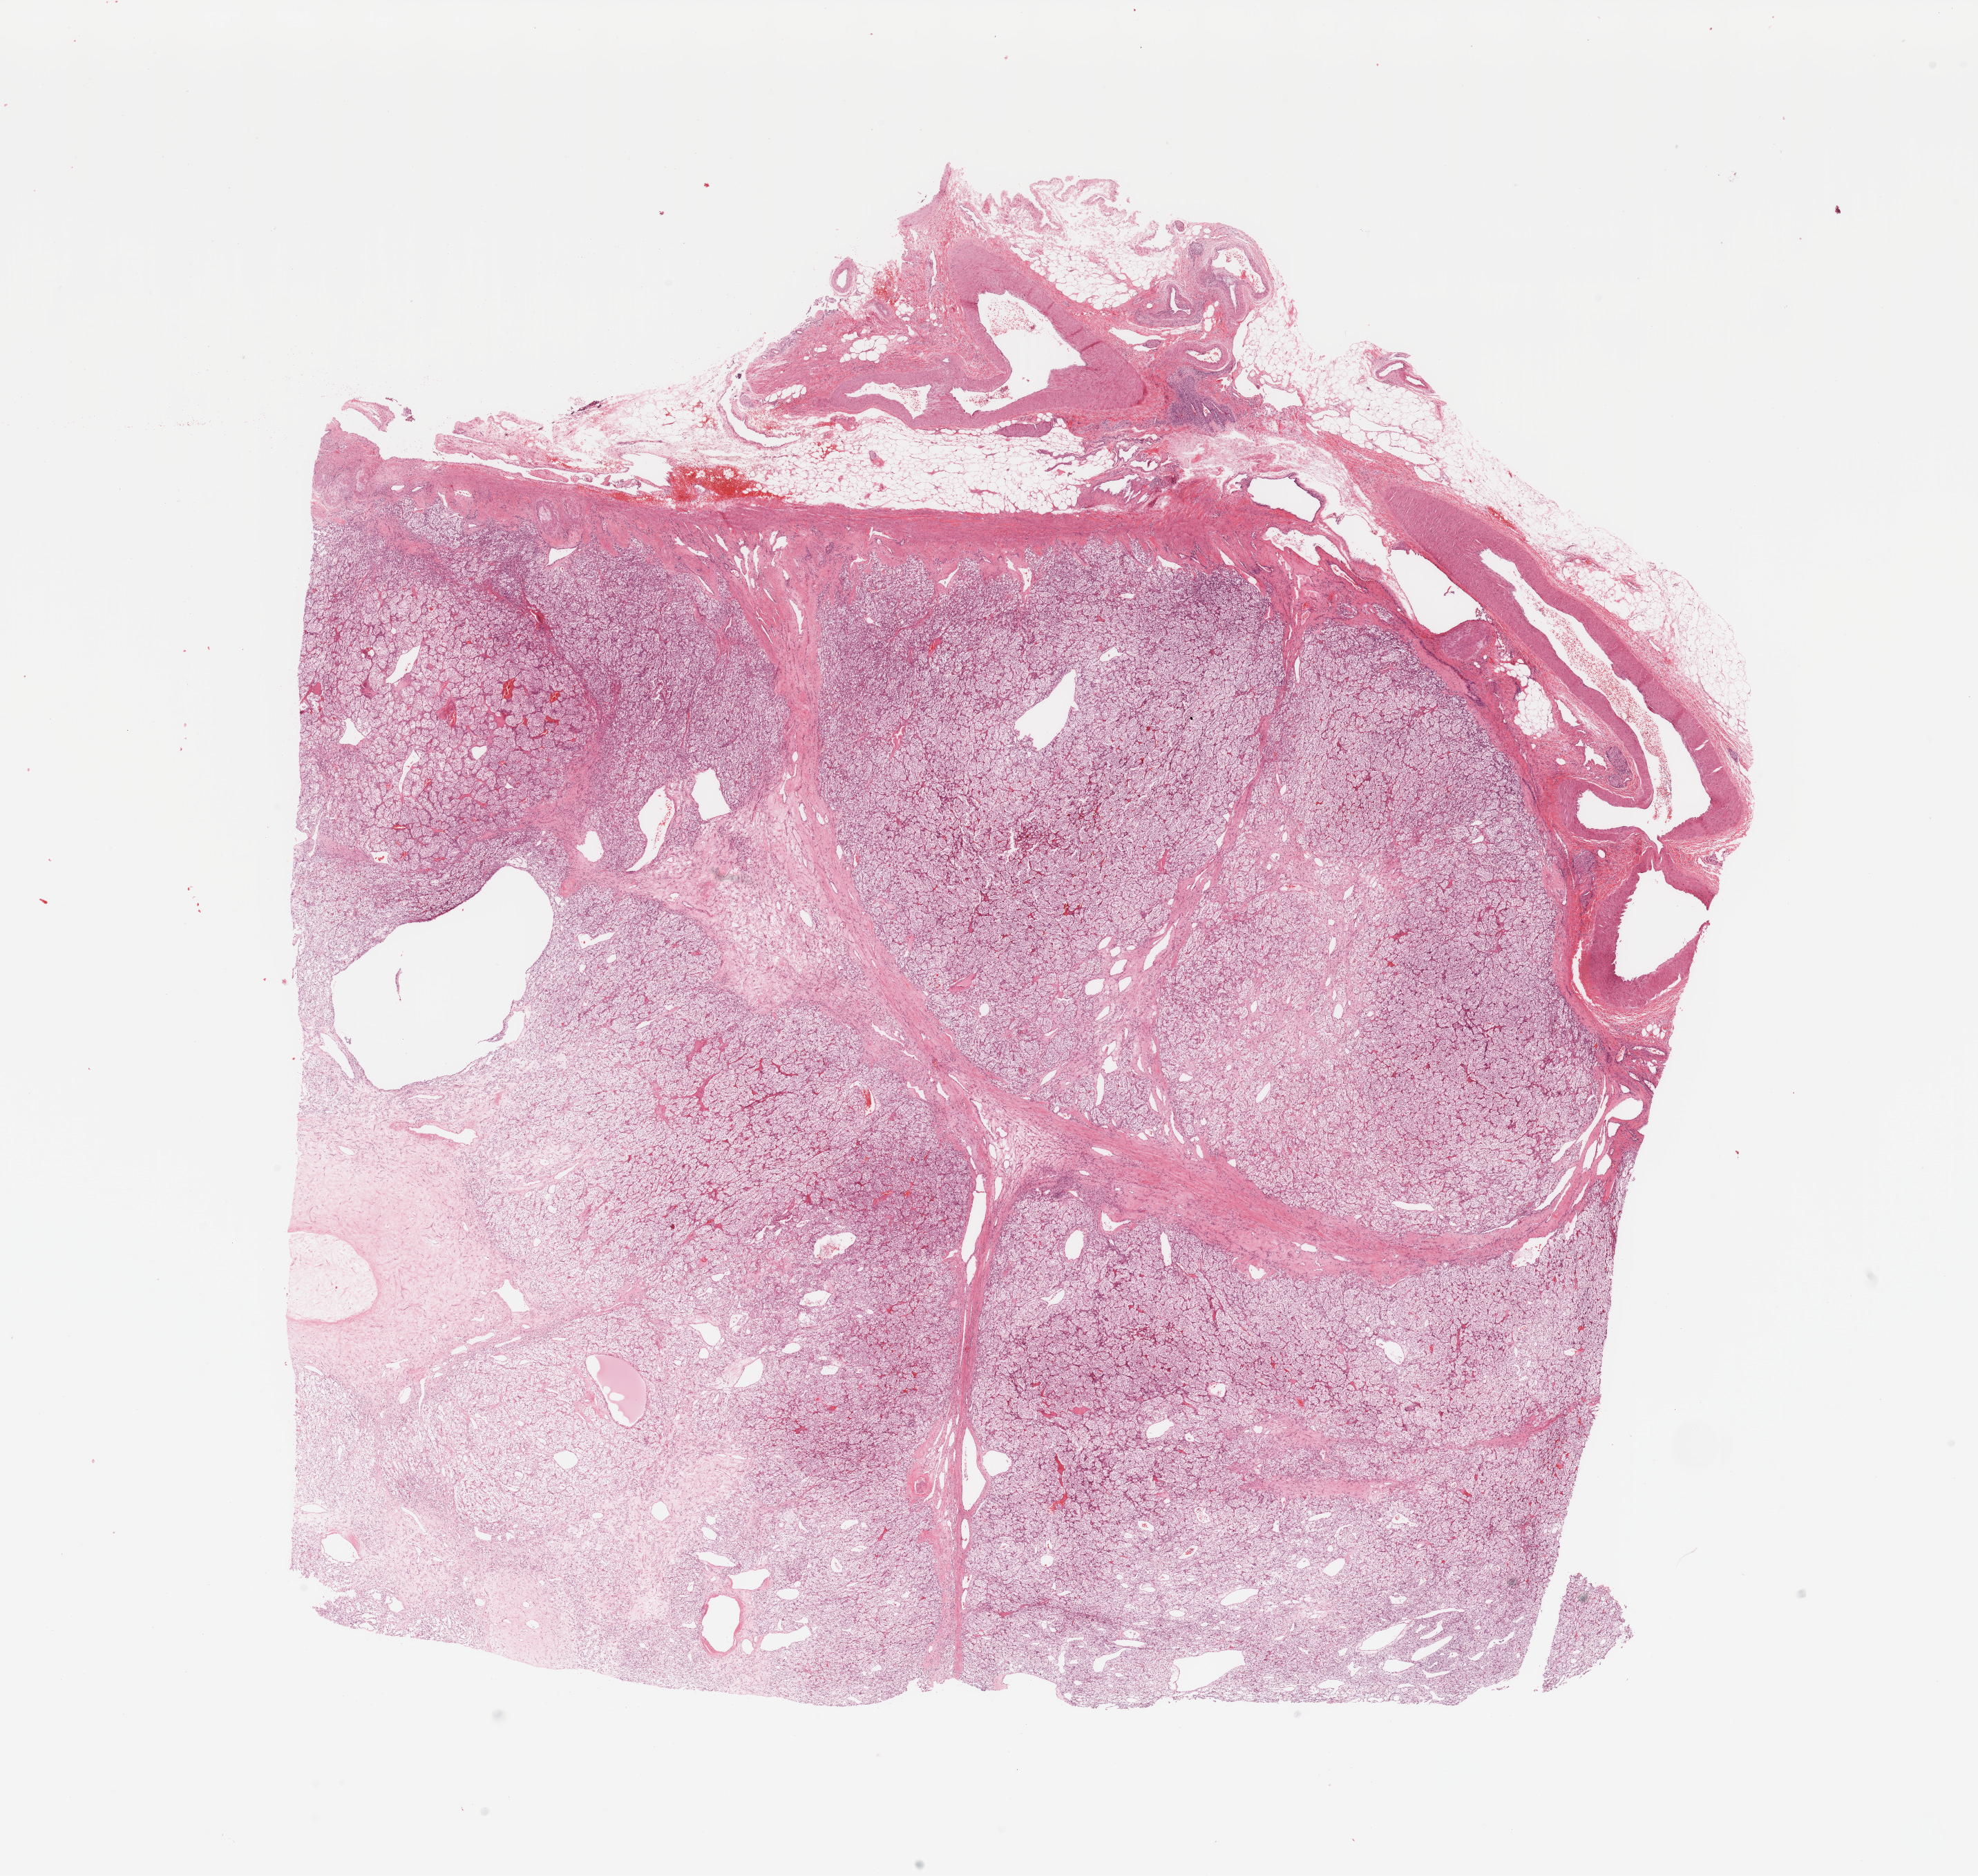
H&E whole-slide image, low-resolution overview of the scanned area, about 22.6 x 21.5 mm (from a 20x scan). Kidney, tumour tissue. Female, 57 y/o. Histologic grade: G1 (well differentiated).
Diagnosis: Renal cell carcinoma, NOS.